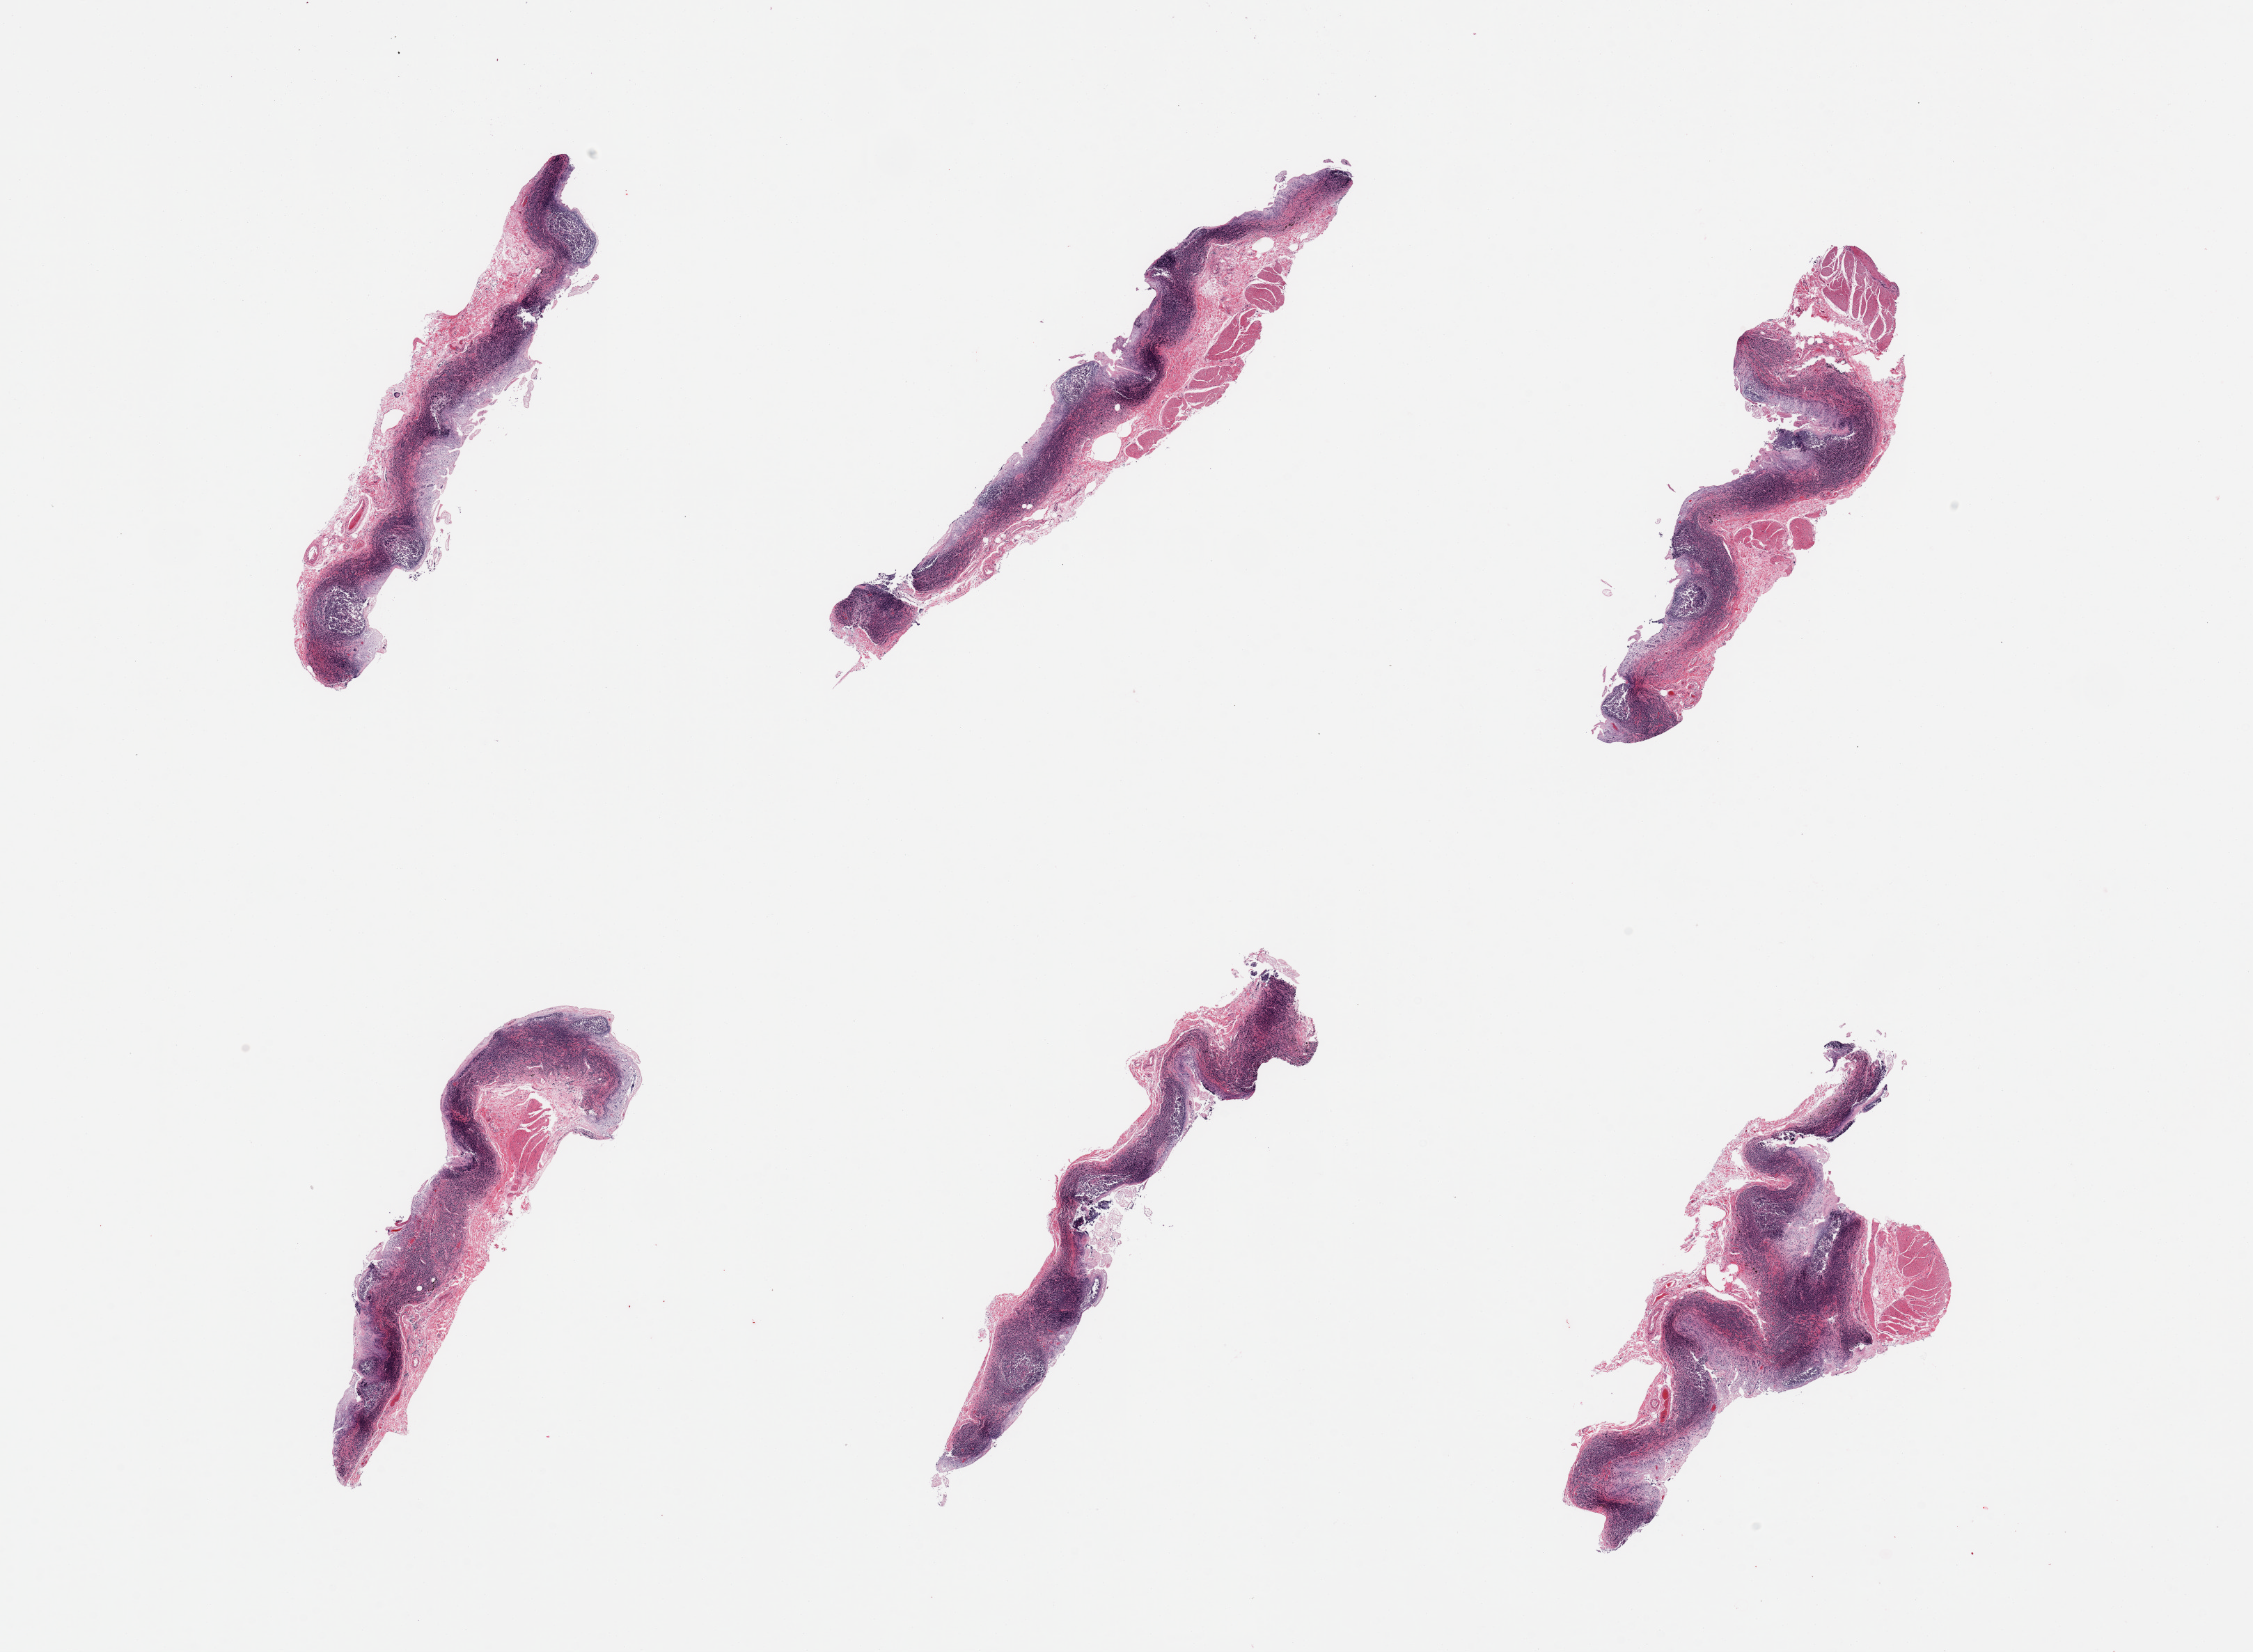
Haematoxylin and eosin whole-slide image, brightfield, shown as a low-resolution overview of the whole scanned area (about 25.6 x 18.8 mm, acquisition: 20x scan), PAXgene-fixed paraffin-embedded (PFPE) section, sampled site (target tissue): ileum, tissue donor sample. Donor: male.
Reviewer comment on this tissue sample: 6 pieces; partly autolyzed, but plentiful lymphoid tissue; variable amounts of muscularis propria in 4 pieces.